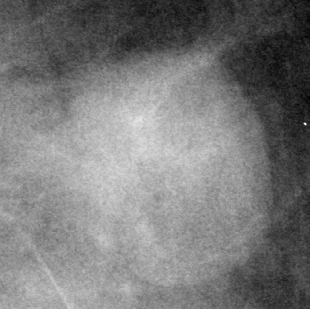
Cropped region of a digitized screen-film mammogram centred on a radiologist-marked abnormality, left breast, CC view, BI-RADS breast density category 2 (scale 1–4).
Marked abnormality: mass, shape oval, margins circumscribed; BI-RADS assessment category 3; pathology (as recorded): benign.